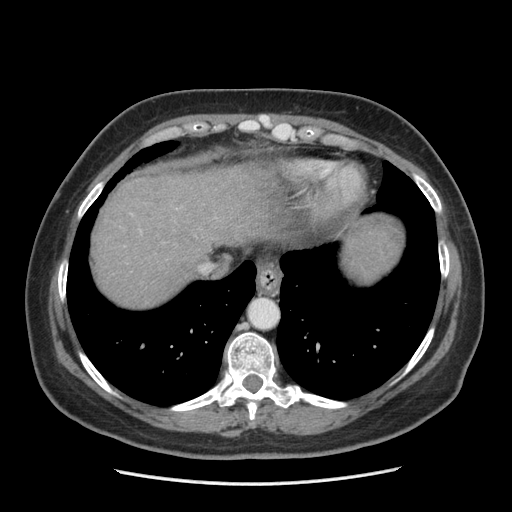
Contrast-enhanced abdominal CT (liver protocol), one axial slice. Slice 170 of 185 in the series (ordered by position). Soft-tissue window (W 400 / L 40 HU). 2.5 mm slice thickness. 512 × 512 image matrix, field of view 360 × 360 mm. From the clinical record (not read from this slice): diagnosis: hepatocellular carcinoma (patient treated with transarterial chemoembolisation; whether this scan precedes or follows treatment is not stated here); TNM stage (as recorded): Stage-I; Child-Pugh class: A.
Outlined on this slice (semi-automatic segmentation, software-assisted and operator-edited):
- liver parenchyma outside the tumour (the mass and vessels are separate outlines, so this box may not span the whole liver): bounding box [x1, y1, x2, y2] px = [92, 162, 402, 306]